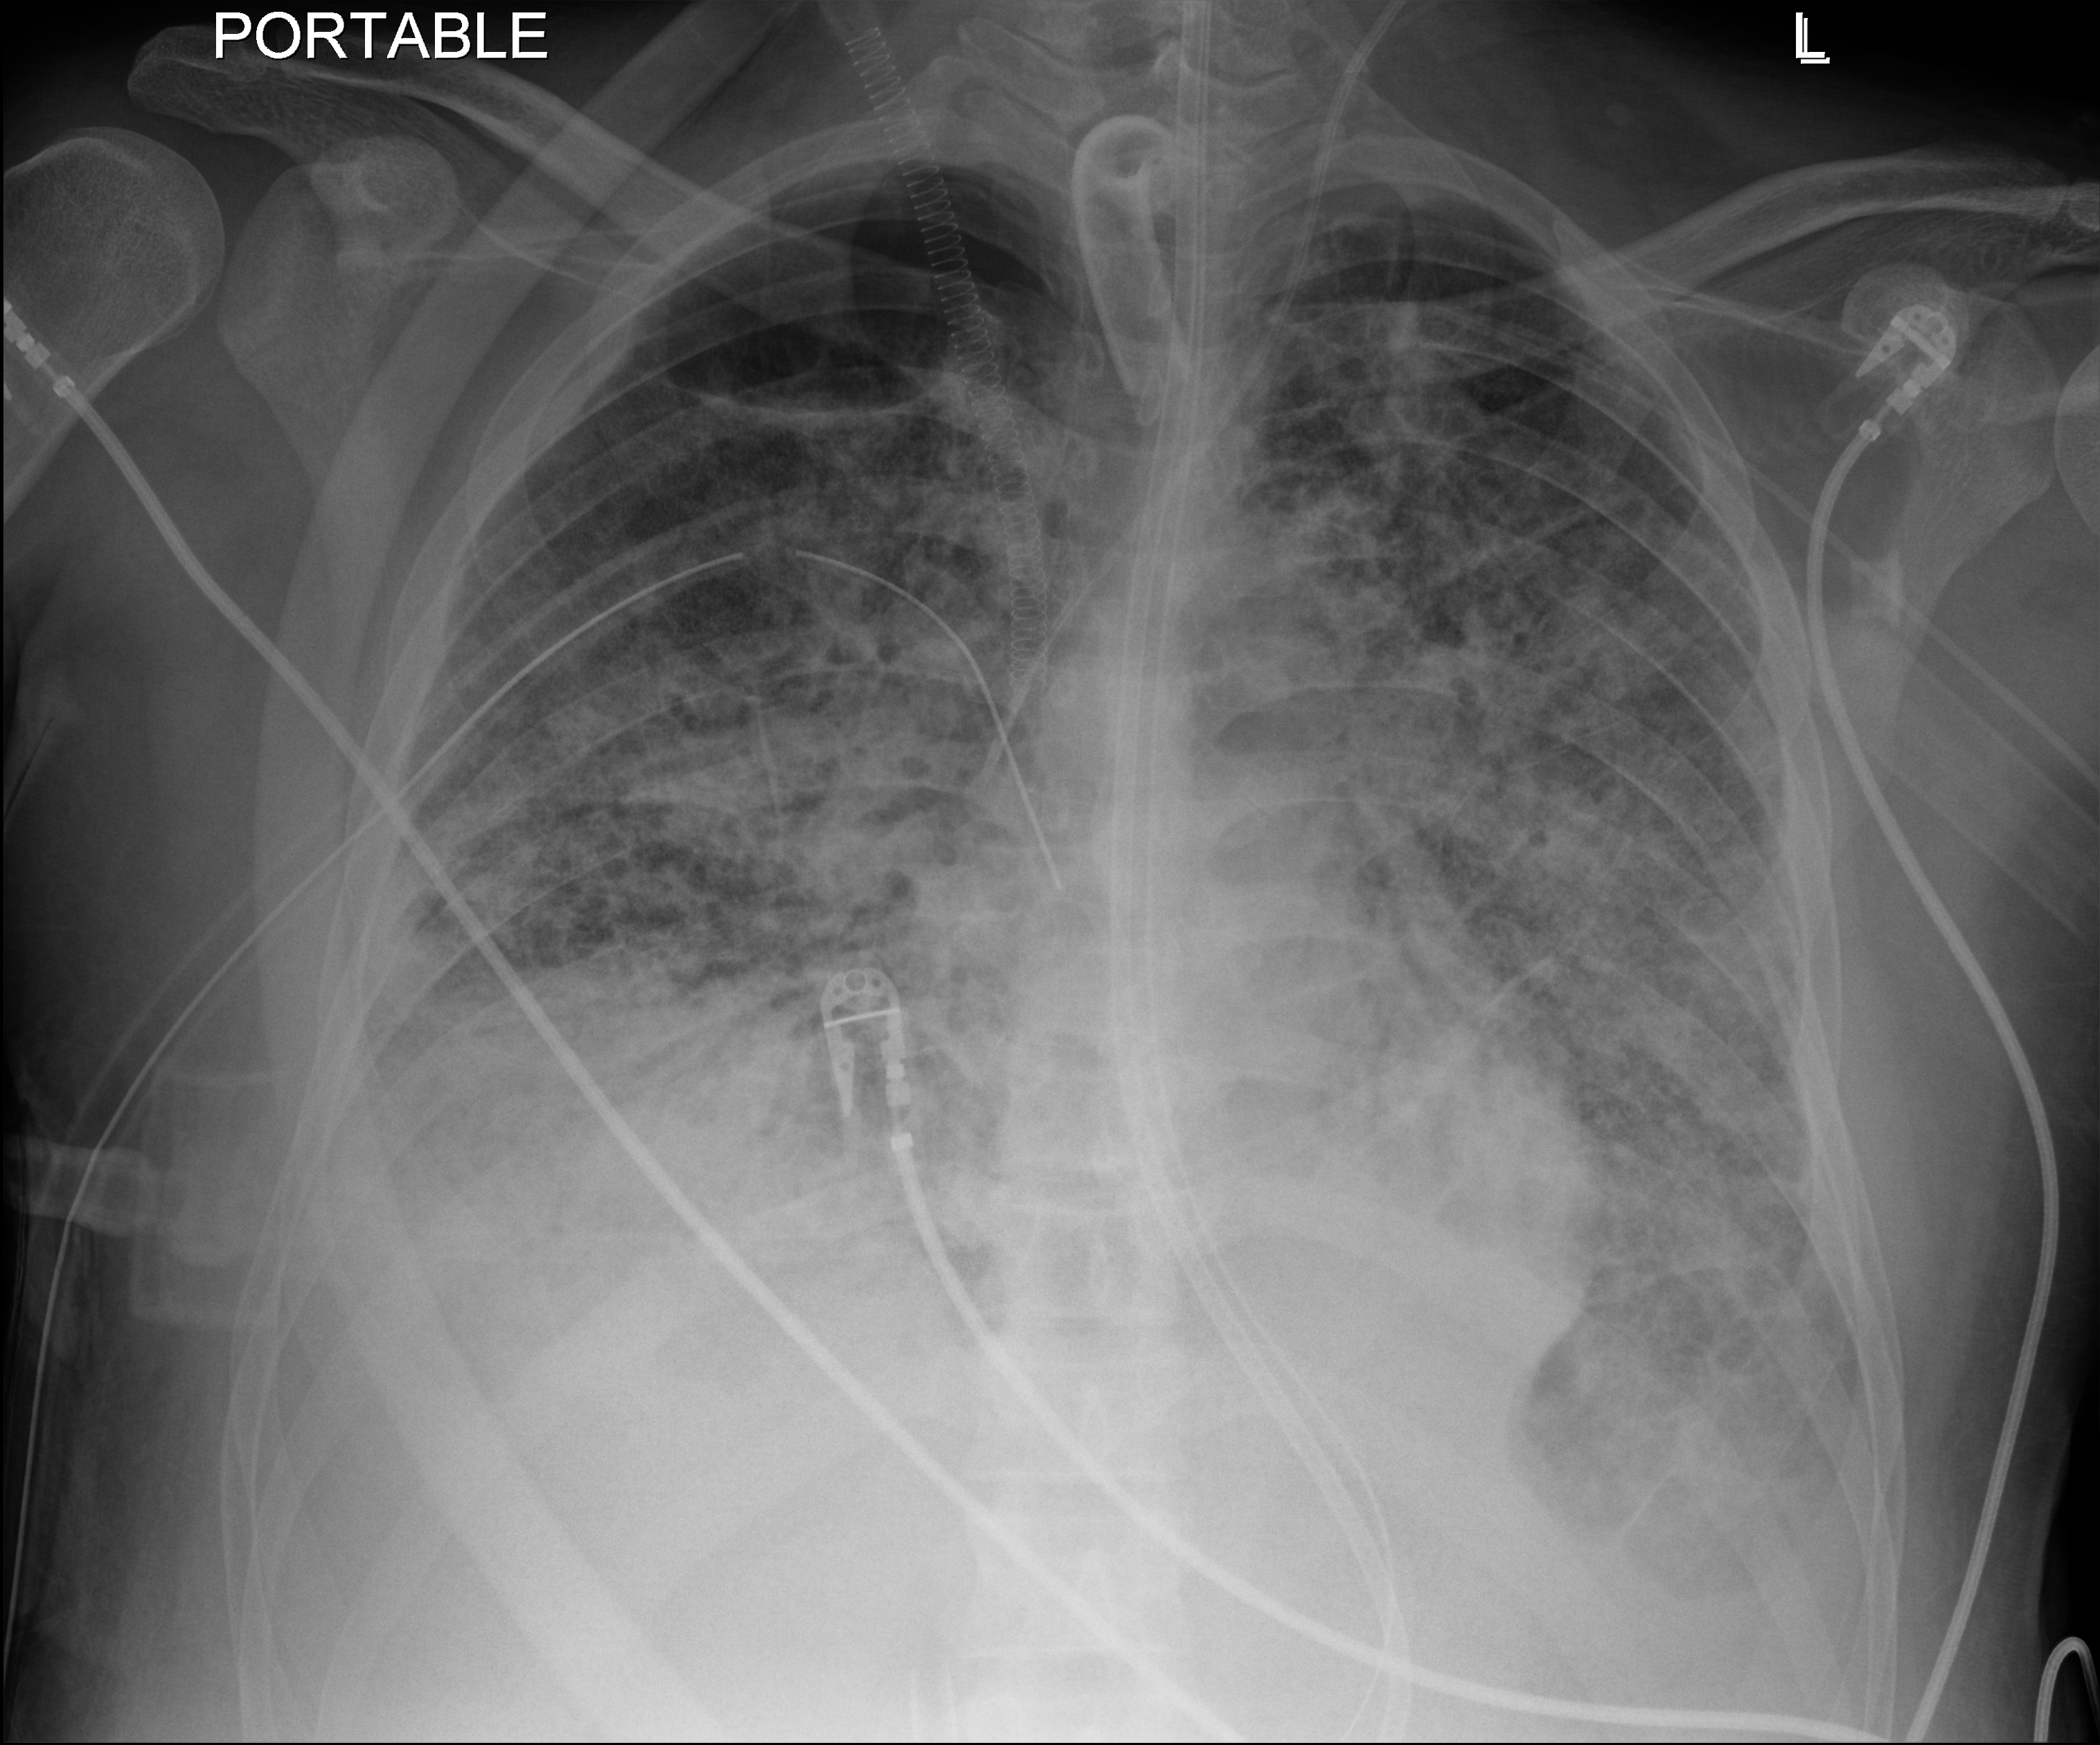
Portable chest radiograph, anteroposterior (AP) projection. Adult patient hospitalised with COVID-19, age 18–59 years.
Admission-level facts for this patient (not findings on this image; timing relative to this image not recorded):
- admitted to intensive care during this hospital stay: yes